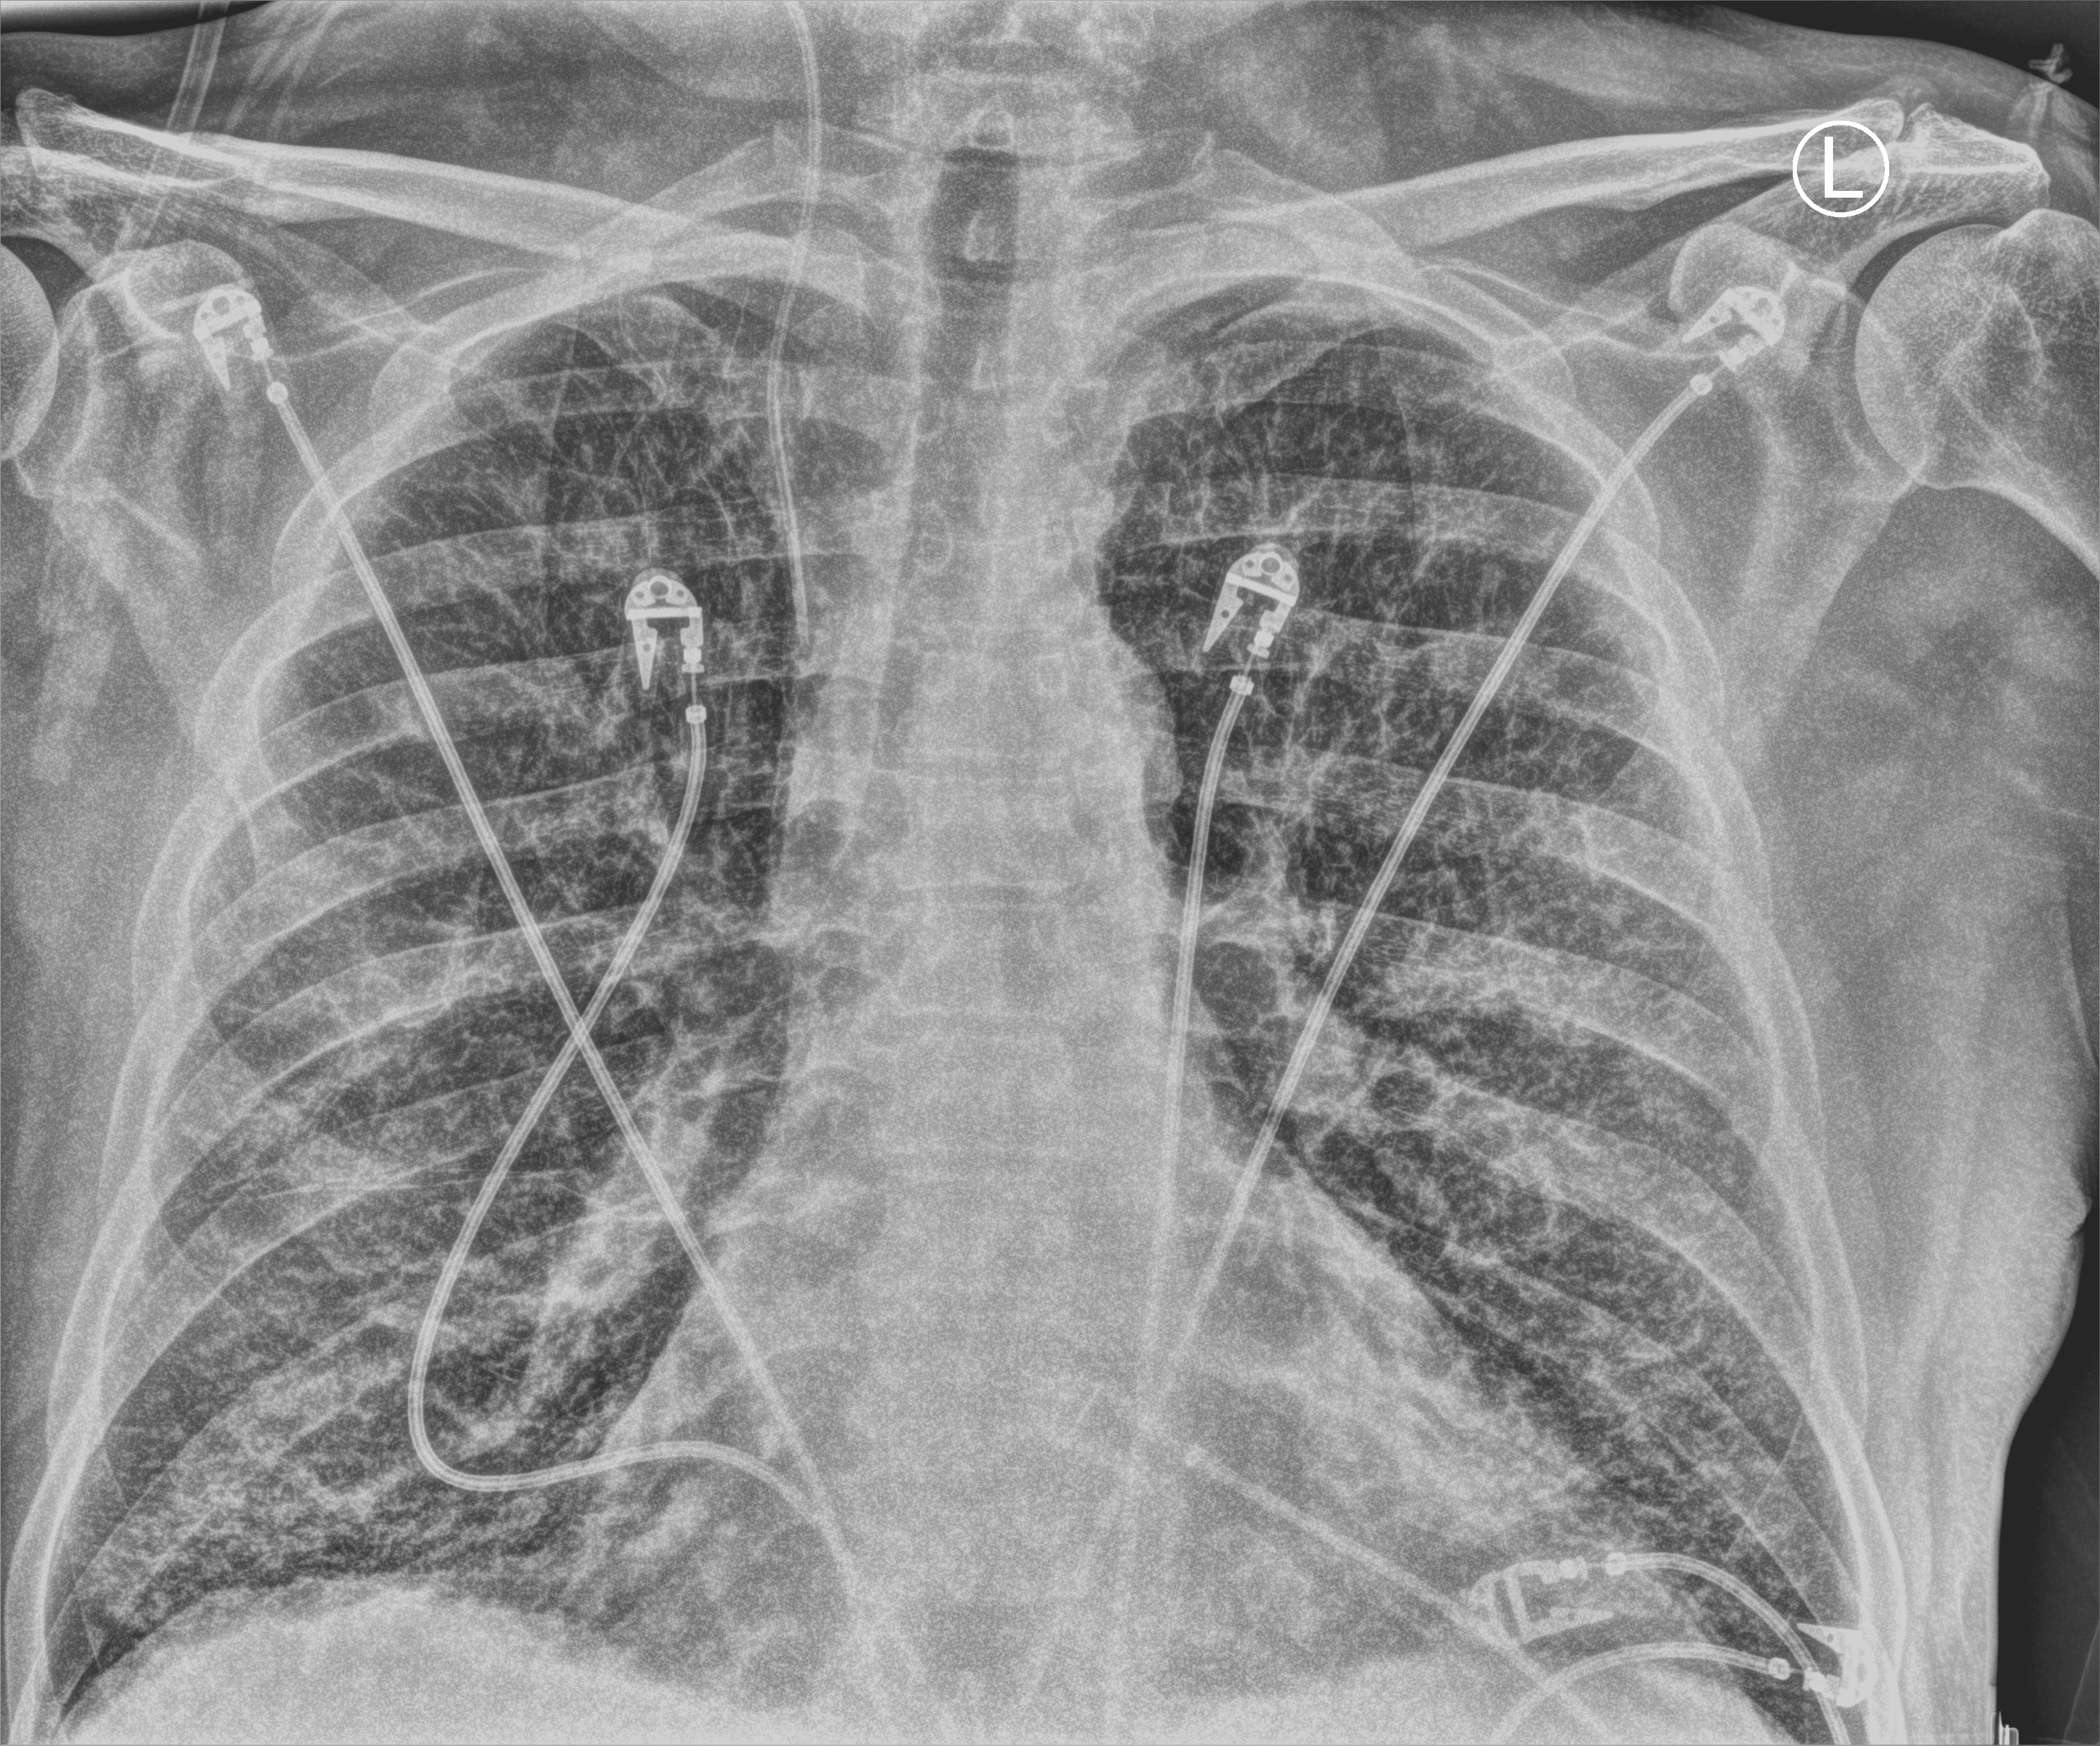
Chest X-ray (portable); anteroposterior (AP) projection. Adult patient hospitalised with COVID-19, age 18–59 years.
Admission-level facts for this patient (not findings on this image; timing relative to this image not recorded):
- admitted to intensive care during this hospital stay: yes
- length of hospital stay: 3 days